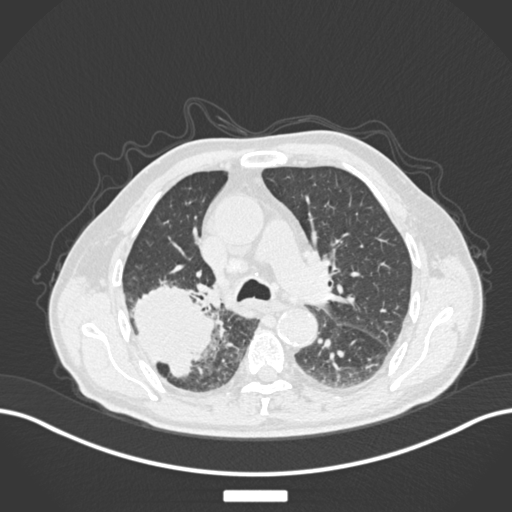
Chest CT, one axial slice; position 114 of 201 along the scan axis; 120 kVp; lung window (W 1500 / L -600 HU); 1 mm slice thickness; 512 × 512 image matrix, field of view 400 × 400 mm. Male patient, age 72 years. Case-level facts recorded for this patient, not image findings: clinical TNM (as recorded): T3 N2 M0.
Outlined on this slice (bounding box drawn by a radiologist):
- lung tumour (recorded histology: adenocarcinoma): bounding box [x1, y1, x2, y2] px = [127, 275, 217, 381]